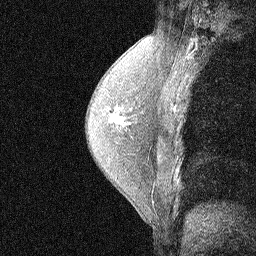
Breast MRI (dynamic contrast-enhanced), one sagittal slice. Slice 37 of 58 in the series (ordered by position). Dynamic contrast-enhanced study with each time point stored as its own series, time point 2 of 3 at this slice position (early post-contrast, ordered by acquisition time). 1.5 T. TE 4.5 ms, TR 11 ms. 2.07 mm slice thickness. 256 × 256 image matrix, field of view 200 × 200 mm. Female patient, age 54 years. From the clinical record (not read from this slice): setting: breast cancer imaged before/during neoadjuvant chemotherapy; receptor status: HR-positive, HER2-negative.
Structures marked on this image (semi-automatic segmentation, software-assisted and operator-edited):
- analysis volume of interest (the breast-tissue region the enhancement analysis was run in; not a lesion): bounding box [x1, y1, x2, y2] px = [92, 89, 149, 186]
- tumour enhancement mask (voxels above the 90 % enhancement threshold inside the analysis volume of interest): [111, 112, 123, 123]